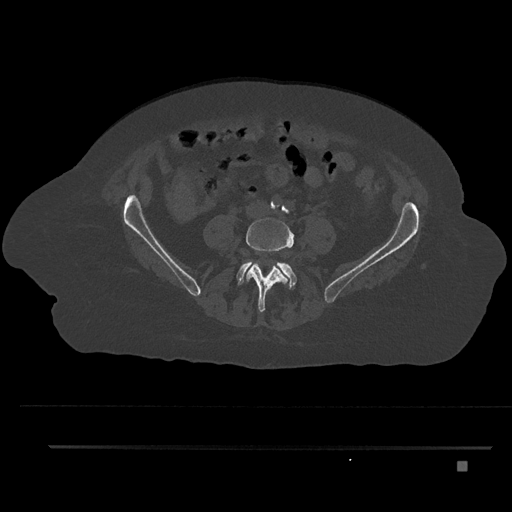
CT including the spine, one axial slice; bone window (W 1800 / L 400 HU); 512 × 512 image matrix. Female patient, age 76 years. Case-level facts recorded for this patient, not image findings: primary cancer: lung; vertebrae with lytic lesions (as recorded): T11, L3.
Outlined on this slice (semi-automatic segmentation, software-assisted and operator-edited):
- L4 vertebra: box from (x=246, y=218) to (x=296, y=312) px
- L5 vertebra: (x=237, y=261)–(x=297, y=289)